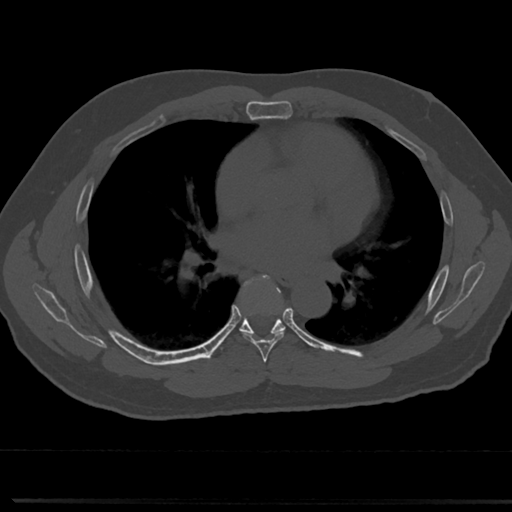
CT including the spine, one axial slice; position 432 of 817 along the scan axis; 120 kVp; bone window (W 1800 / L 400 HU); 0.5 mm slice thickness; 512 × 512 image matrix. Patient: male, 61 years. From the clinical record (not read from this slice): primary cancer: prostate.
Annotated regions visible in this slice (semi-automatically segmented with operator editing):
- T5 vertebra: bounding box [x1, y1, x2, y2] px = [265, 370, 271, 376]
- T6 vertebra: [237, 276, 290, 356]
- T7 vertebra: [241, 326, 283, 334]